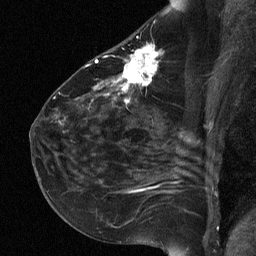
Breast MRI (dynamic contrast-enhanced), one sagittal slice. Slice 36 of 64 in the series (ordered by position). Dynamic contrast-enhanced study with each time point stored as its own series, time point 2 of 3 at this slice position (early post-contrast, ordered by acquisition time). 1.5 T. TE 4.8 ms, TR 27 ms. 2 mm slice thickness. 256 × 256 image matrix. Female patient, age 51 years. Case-level facts recorded for this patient, not image findings: setting: breast cancer imaged before/during neoadjuvant chemotherapy; receptor status: HR-positive, HER2-negative.
Structures marked on this image (semi-automatic segmentation, software-assisted and operator-edited):
- analysis volume of interest (the breast-tissue region the enhancement analysis was run in; not a lesion): bounding box (x1, y1, x2, y2) in pixels: (72, 34, 162, 118)
- tumour enhancement mask (voxels above the 90 % enhancement threshold inside the analysis volume of interest): (94, 46, 159, 103)